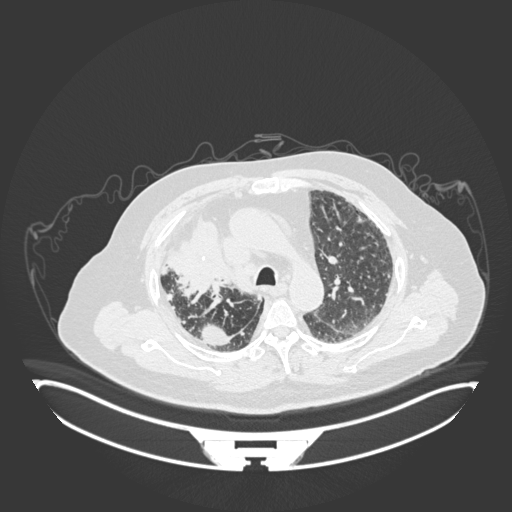
Chest CT, one axial slice. Reconstruction kernel B30f. 120 kVp. Lung window (W 1500 / L -600 HU). 1 mm slice thickness. 512 × 512 image matrix, field of view 500 × 500 mm. Patient: male, 69 years. Case-level facts recorded for this patient, not image findings: clinical TNM (as recorded): T4 N3 M1.
Outlined on this slice (rectangle marked by the reading radiologist):
- lung tumour (recorded histology: adenocarcinoma): box from (x=168, y=218) to (x=235, y=302) px